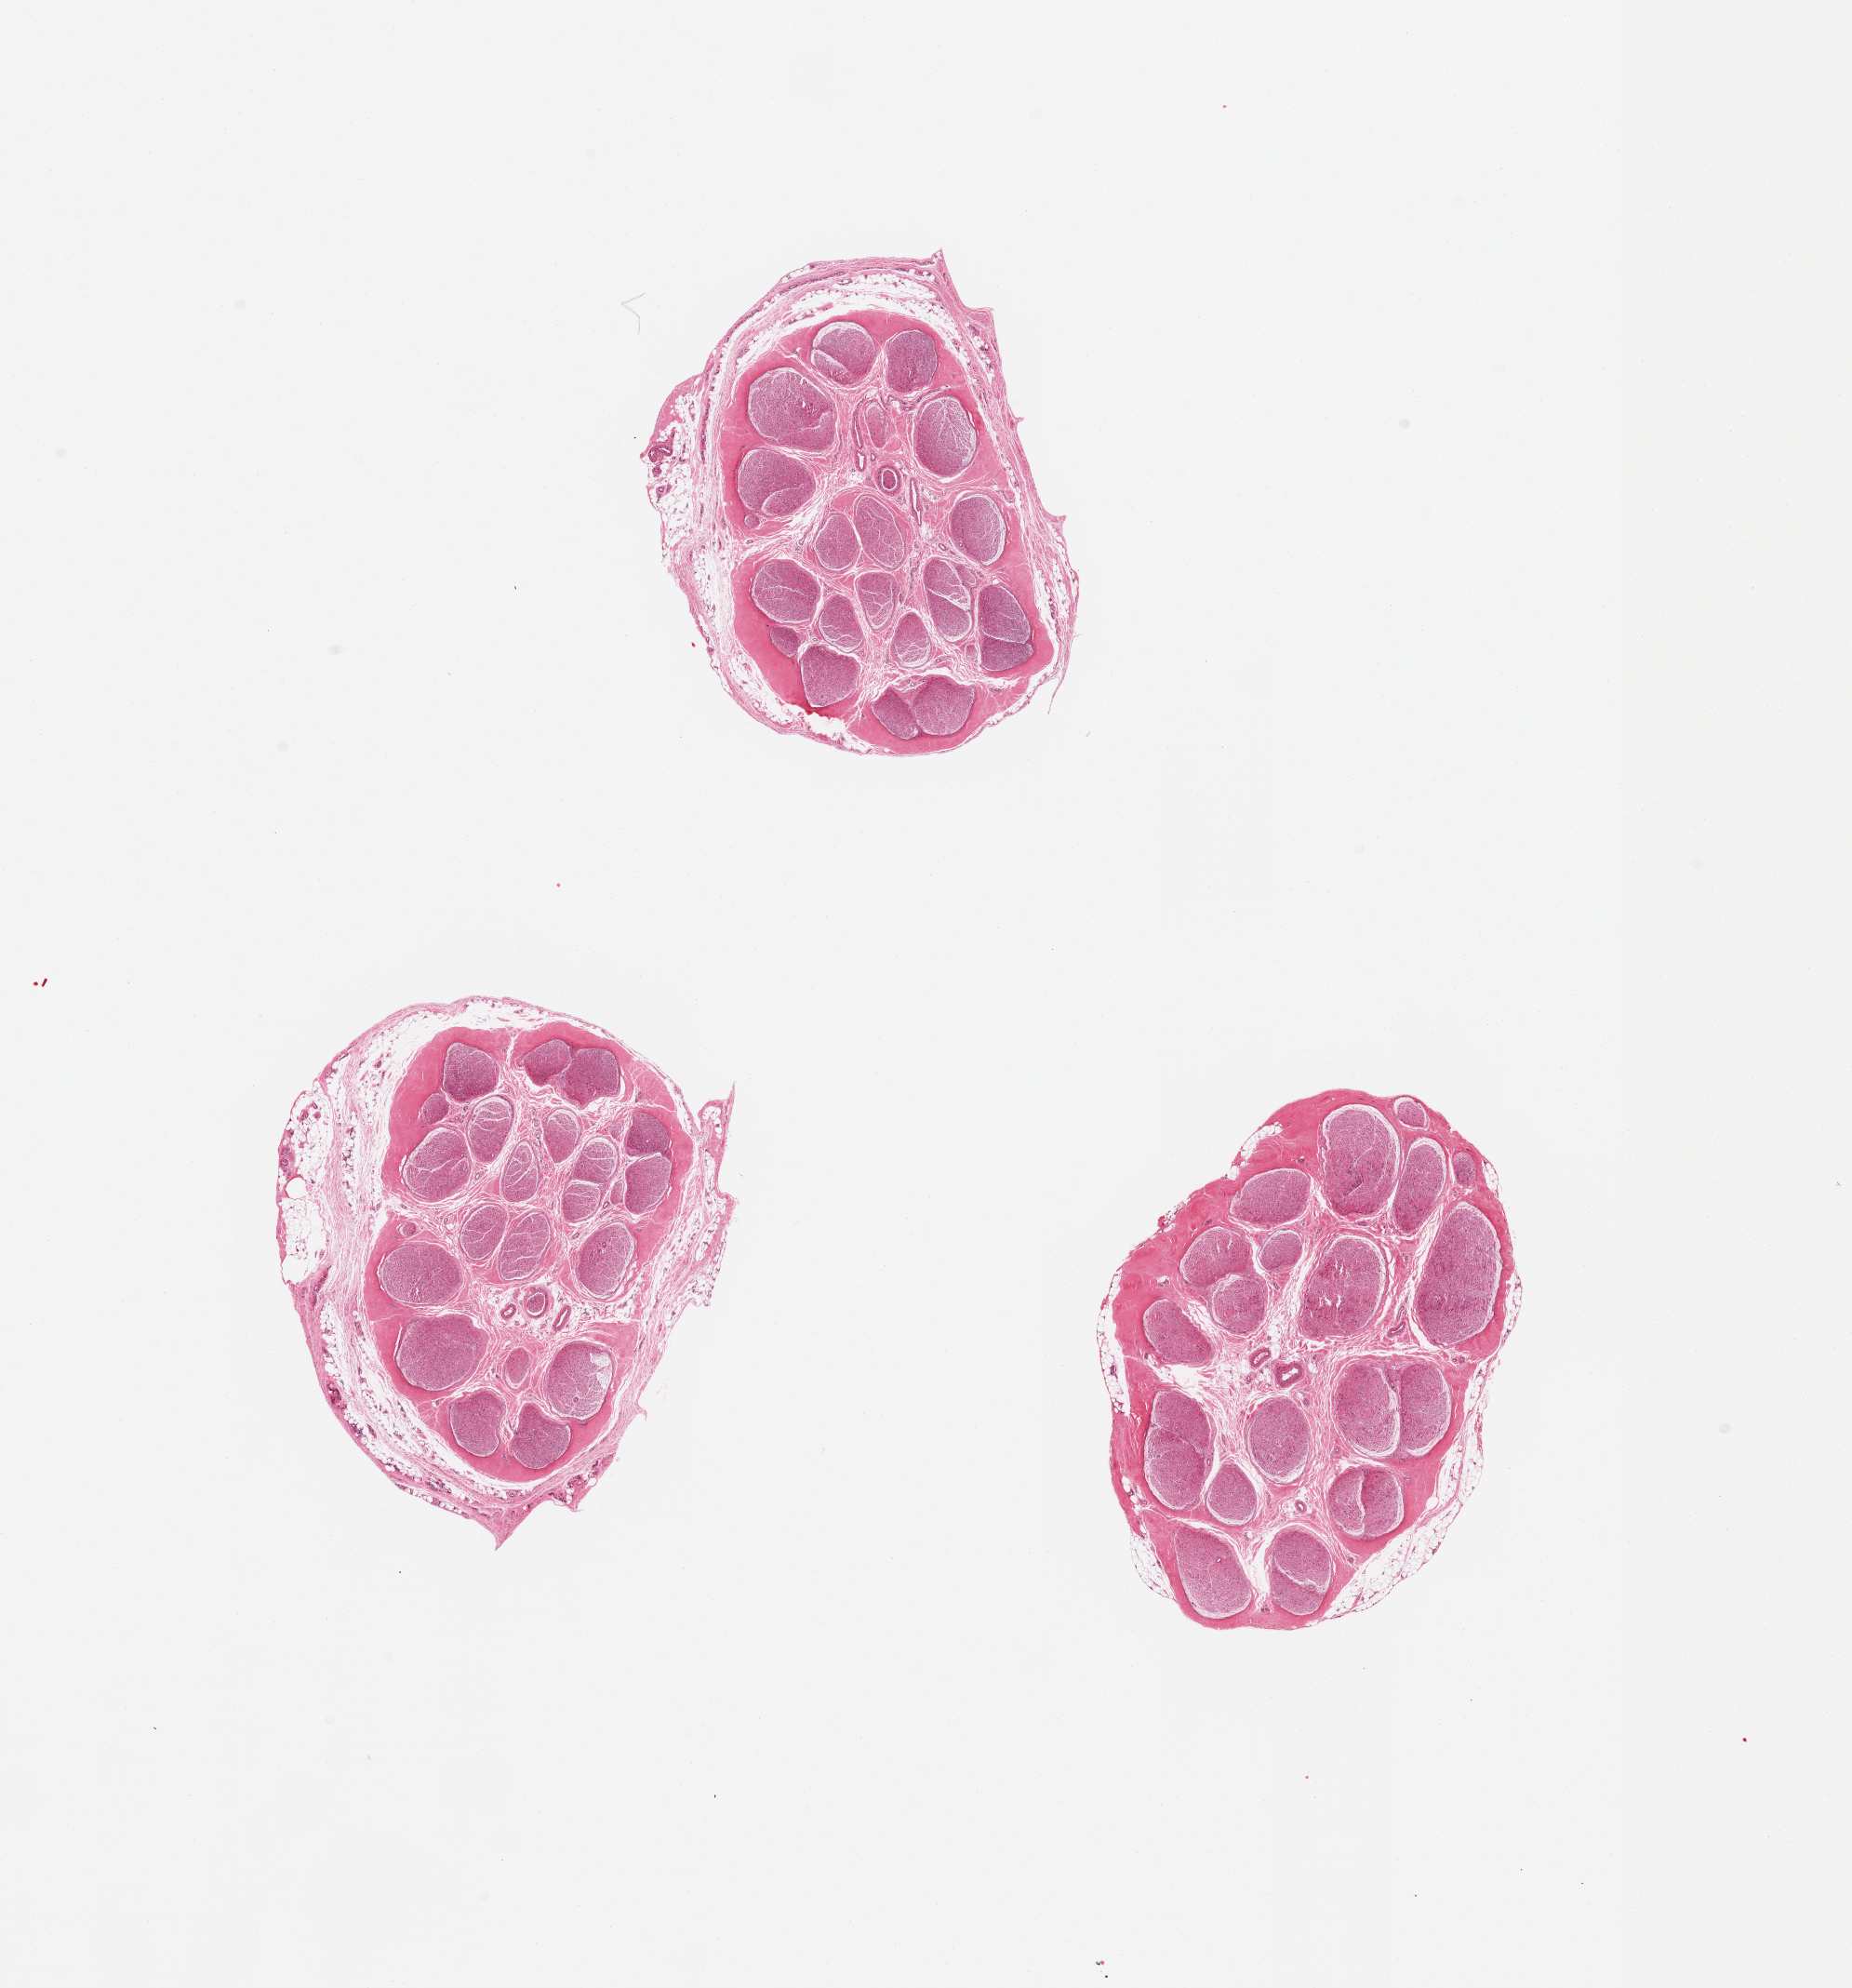
Hematoxylin and eosin (H&E) whole-slide image — low-resolution overview of the scanned area, about 15.8 x 16.9 mm (from a 20x scan). PAXgene-fixed, paraffin-embedded tissue. Section of tibial nerve (target tissue). Tissue donor sample. Donor sex: male.
Review note (as recorded): 3 pieces; 1mm epineurium with external fat.